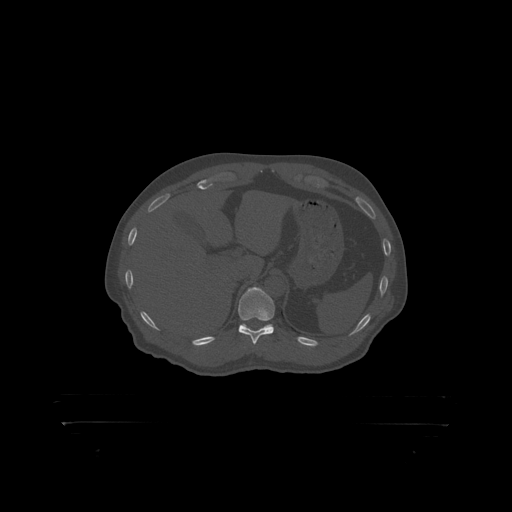
CT including the spine, one axial slice. Slice 374 of 399 in the series (ordered by position). Reconstruction kernel STANDARD. 120 kVp. Bone window (W 1800 / L 400 HU). 512 × 512 image matrix, field of view 650 × 650 mm. Male patient, age 46 years. Case-level facts recorded for this patient, not image findings: primary cancer: skin.
Annotated regions visible in this slice (semi-automatically segmented with operator editing):
- T11 vertebra: box from (x=239, y=288) to (x=276, y=319) px